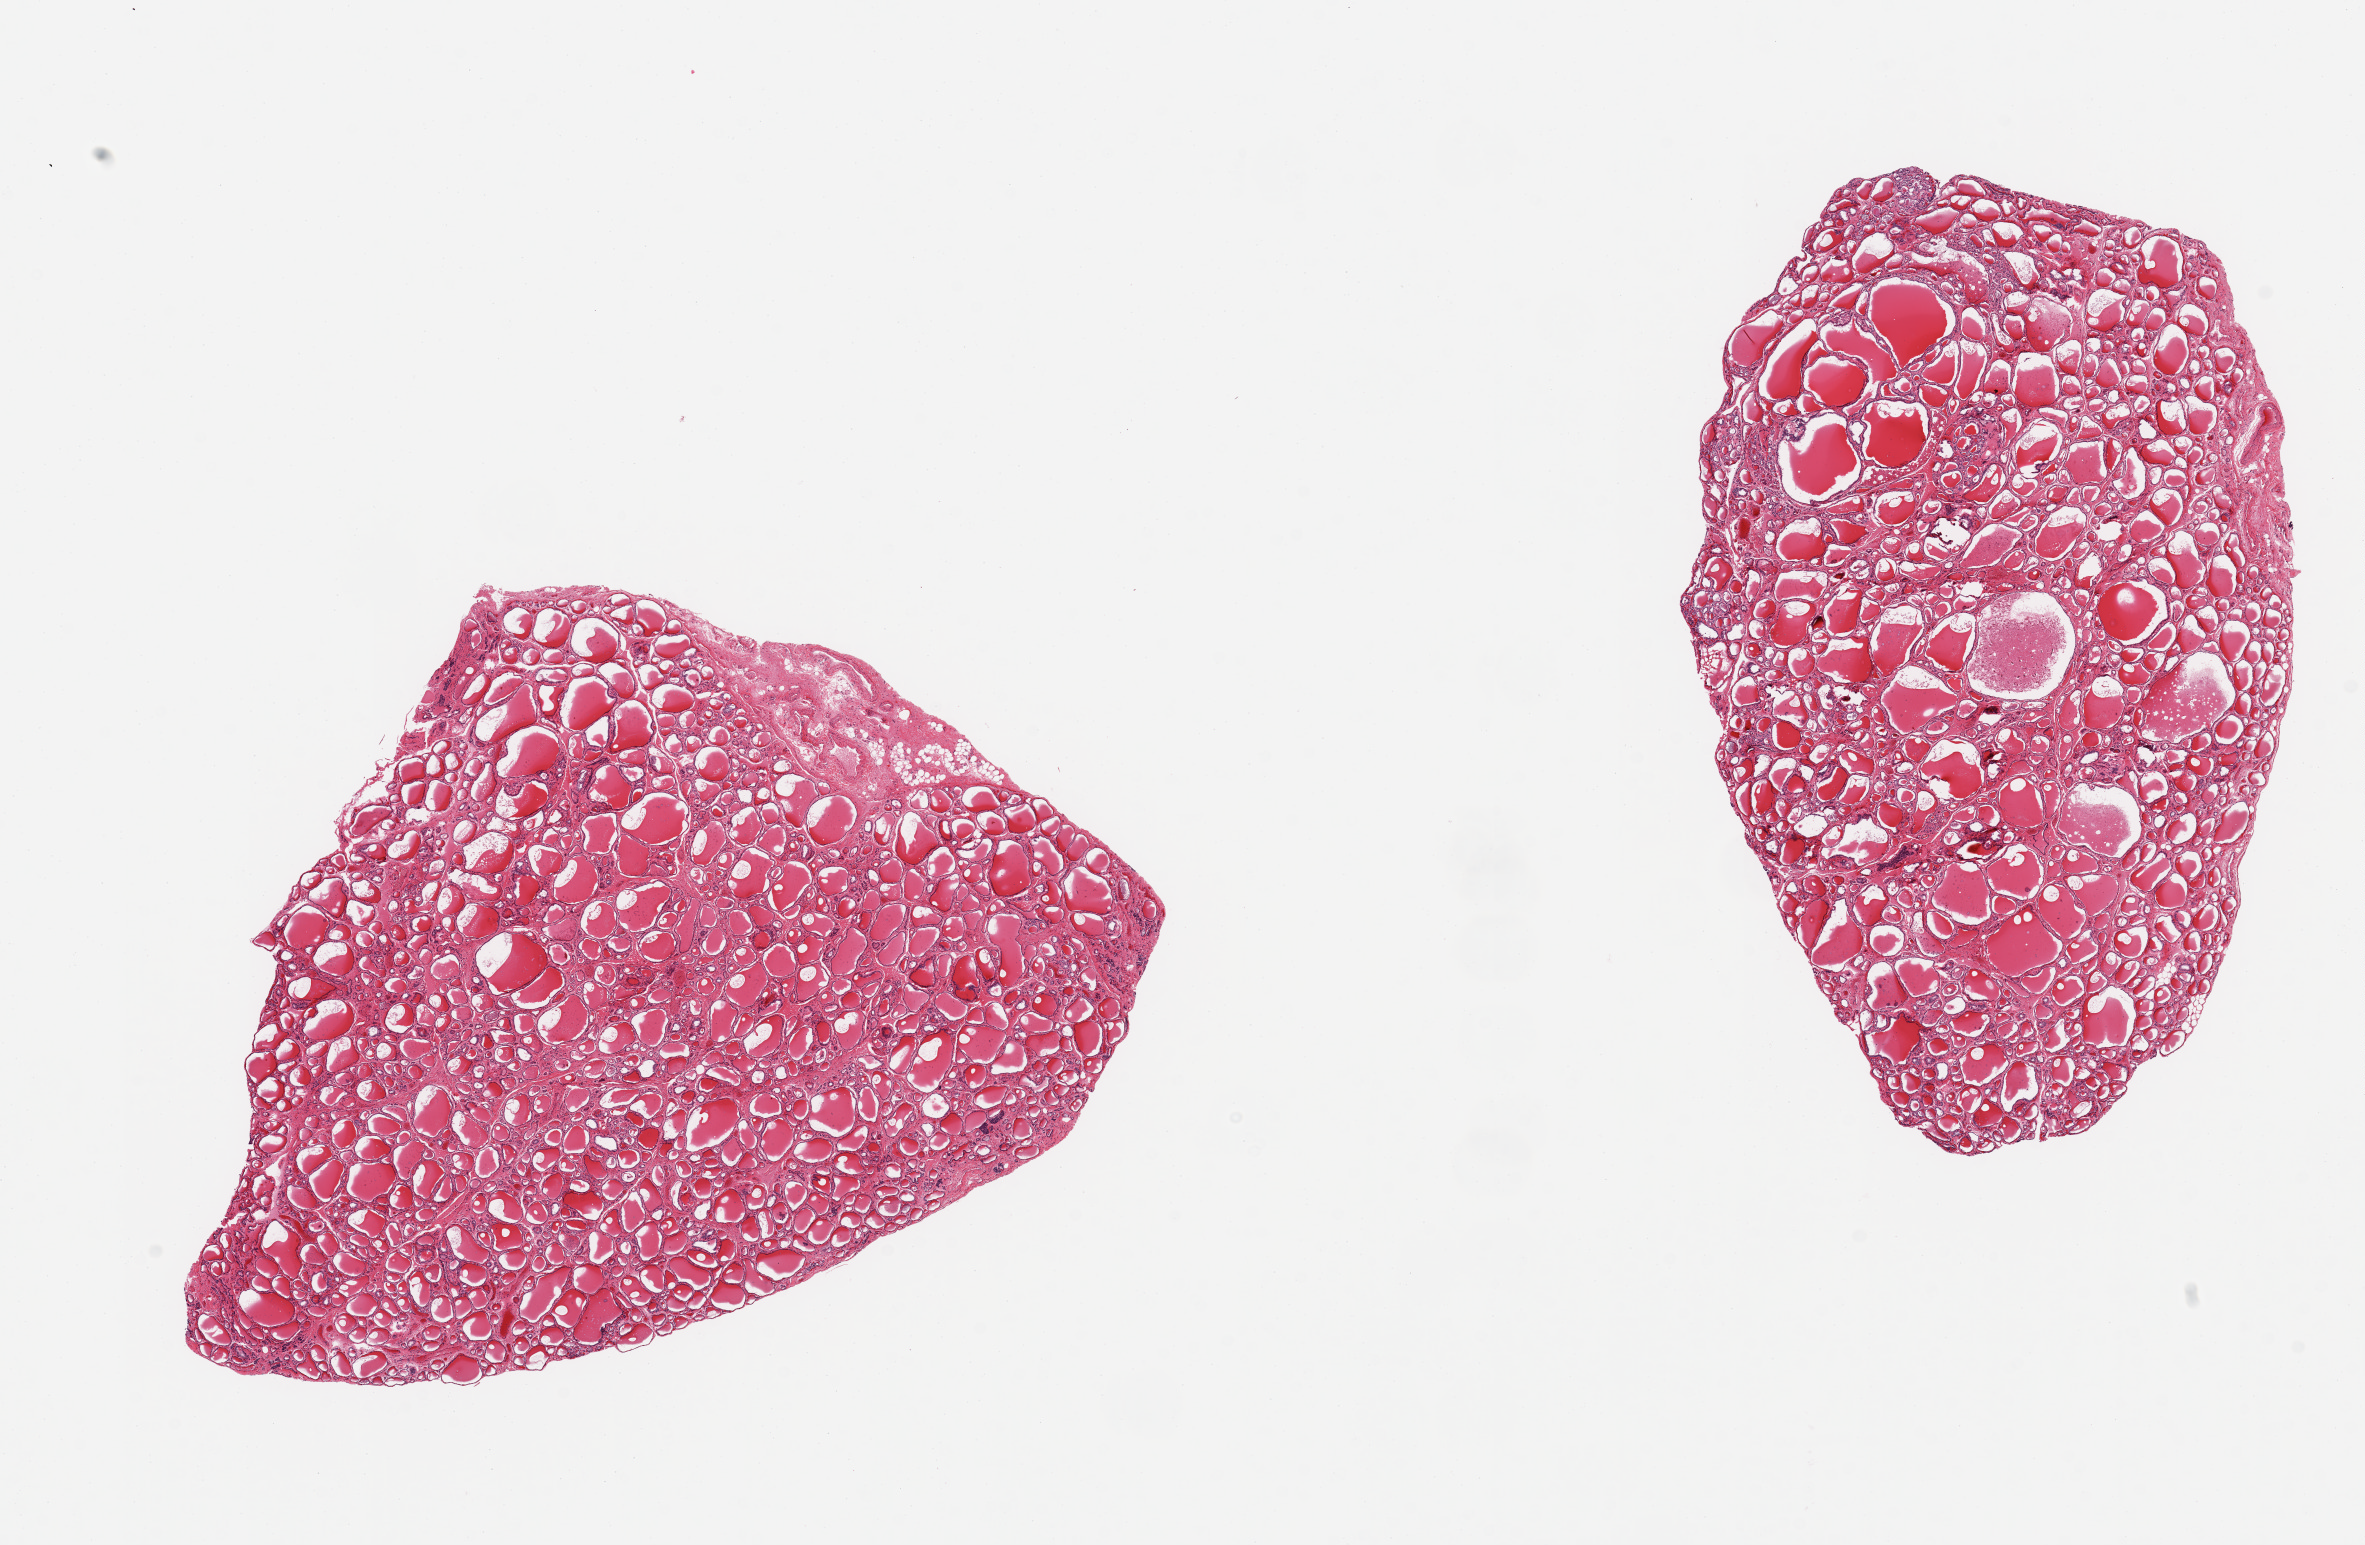
Whole-slide image, H&E stain — low-resolution overview of the scanned area, about 18.7 x 12.2 mm (acquisition: 20x scan). PAXgene-fixed, paraffin-embedded tissue. Section of thyroid (target tissue). Tissue donor sample. Male donor.
Review note (as recorded): 2 pieces, no abnormalitites, focal adhereant fat.